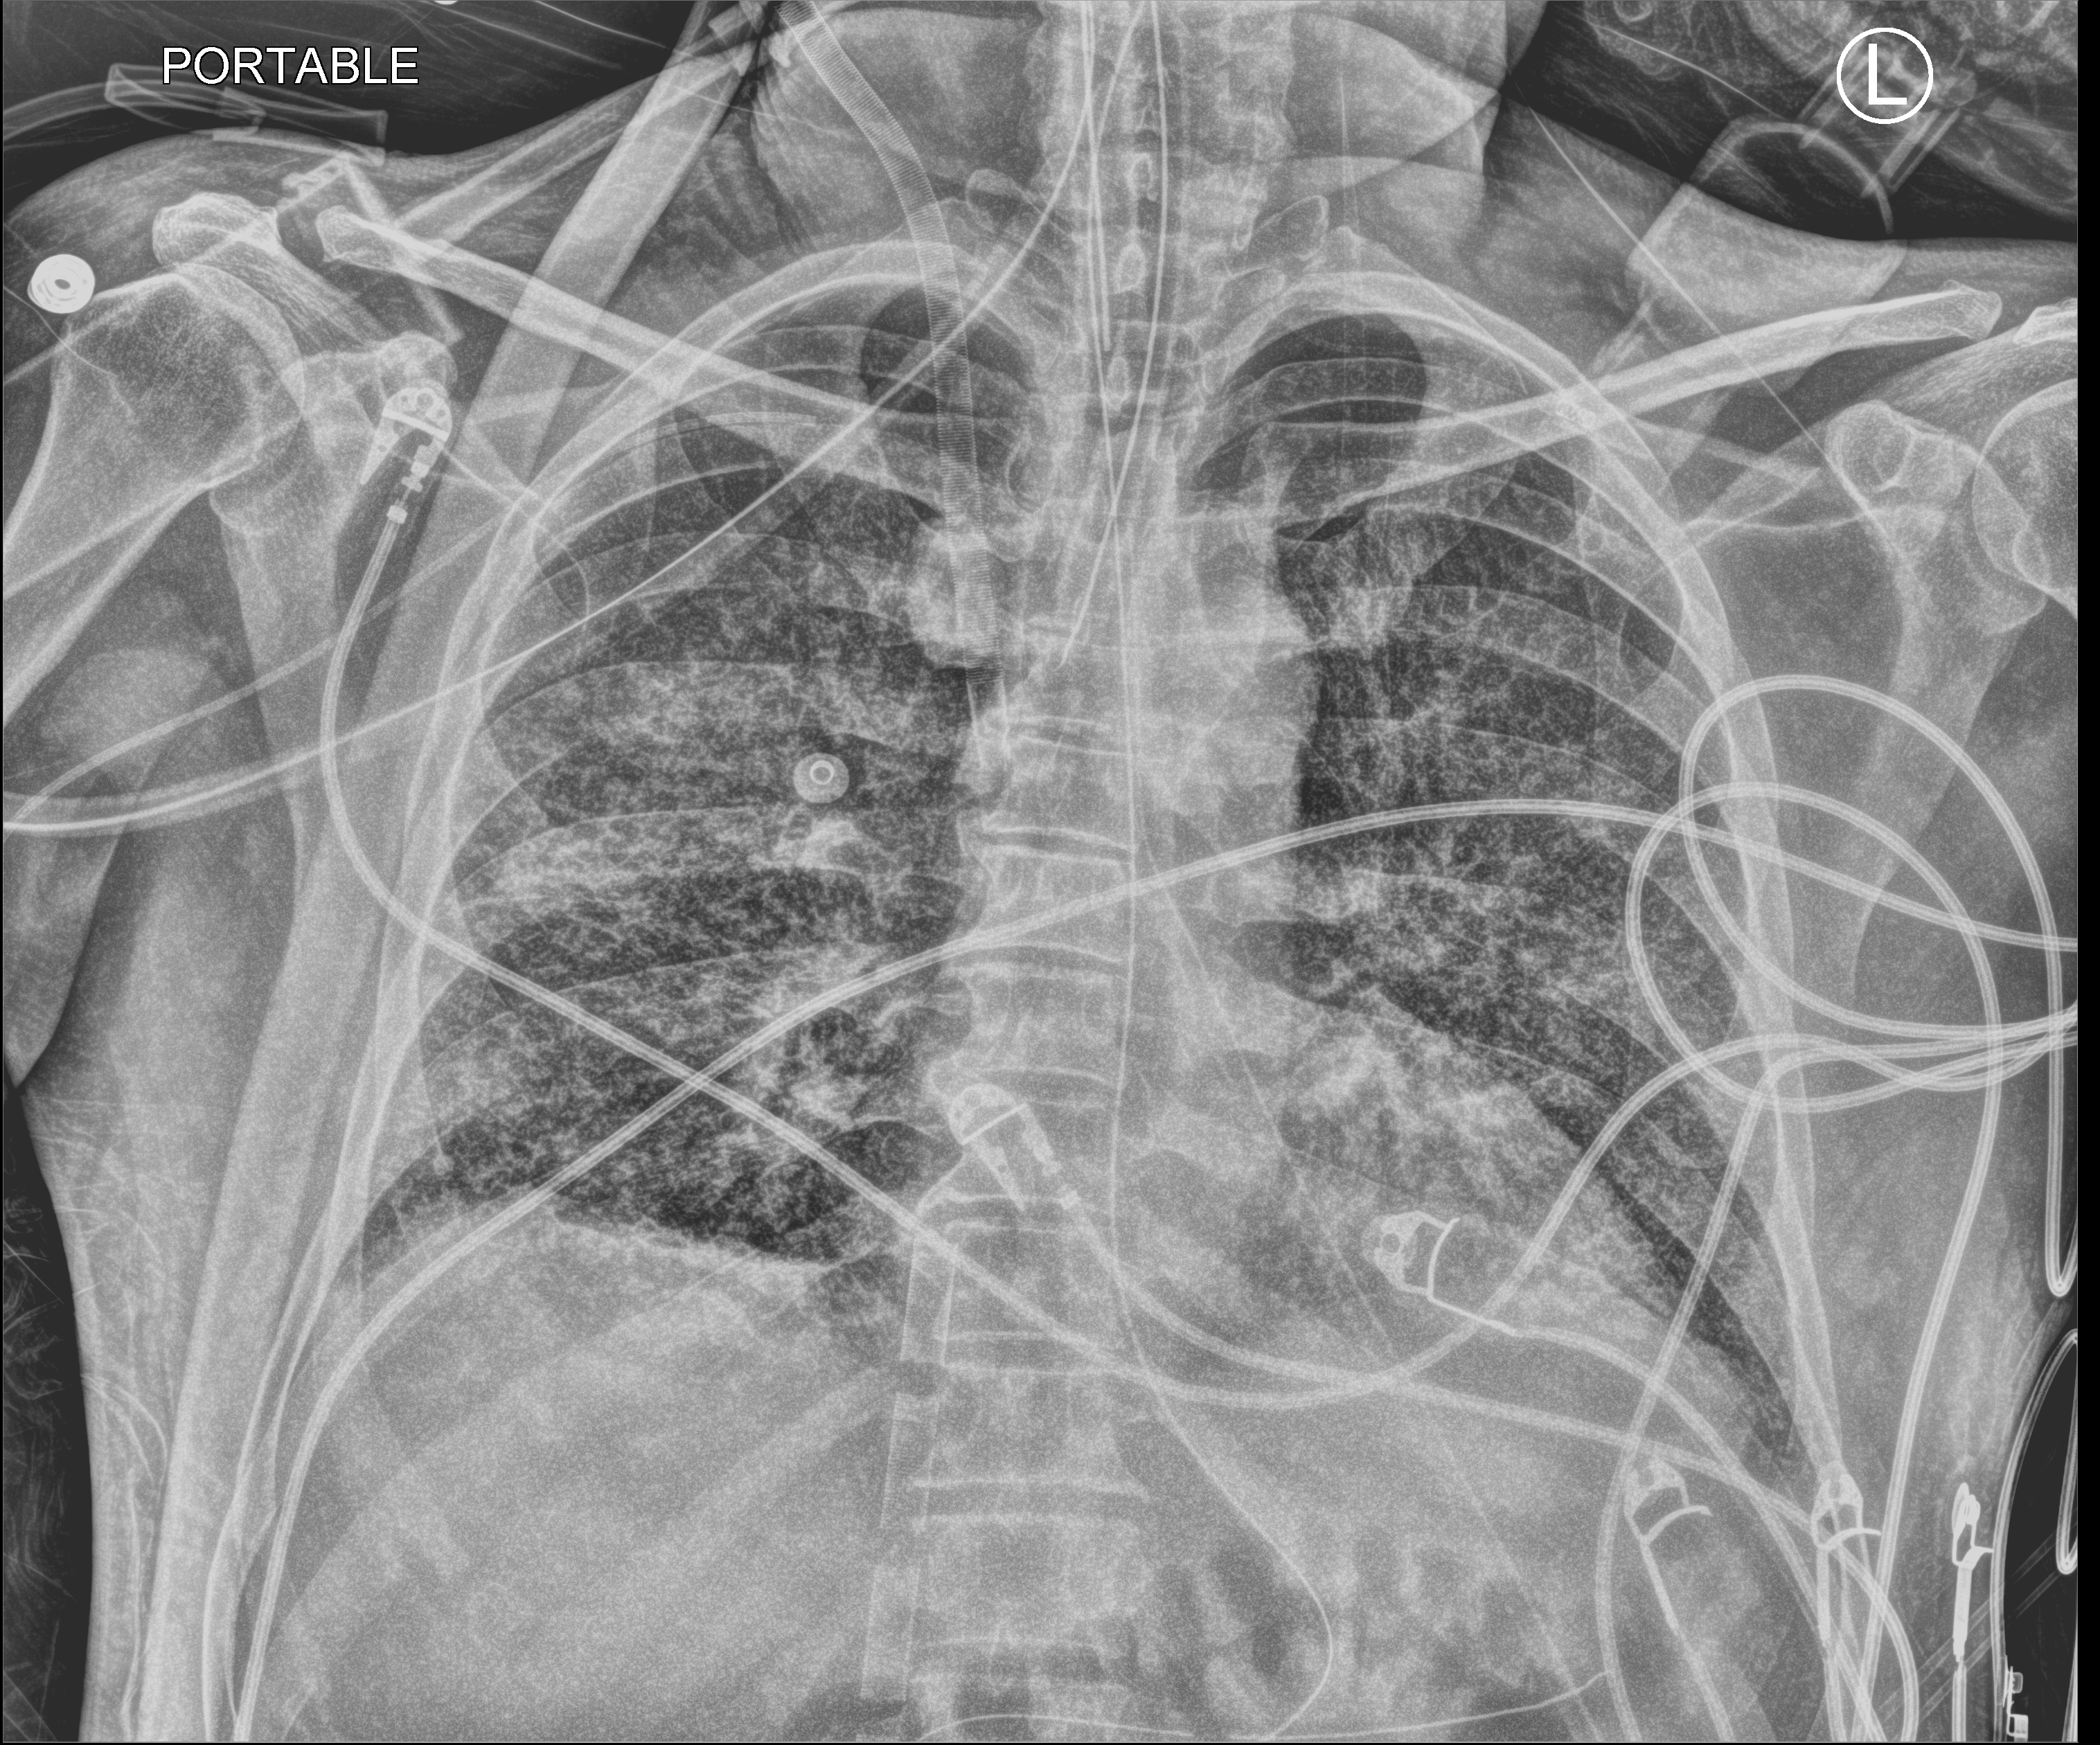
Bedside chest radiograph (computed radiography); anteroposterior (AP) projection. Patient hospitalised with COVID-19; male, aged 18–59 years.
Hospital-stay facts (about this admission, not read from this image; timing relative to this image not recorded): other chronic lung disease (admission record): no; mechanically ventilated during this hospital stay: yes; hypertension (admission record): no.